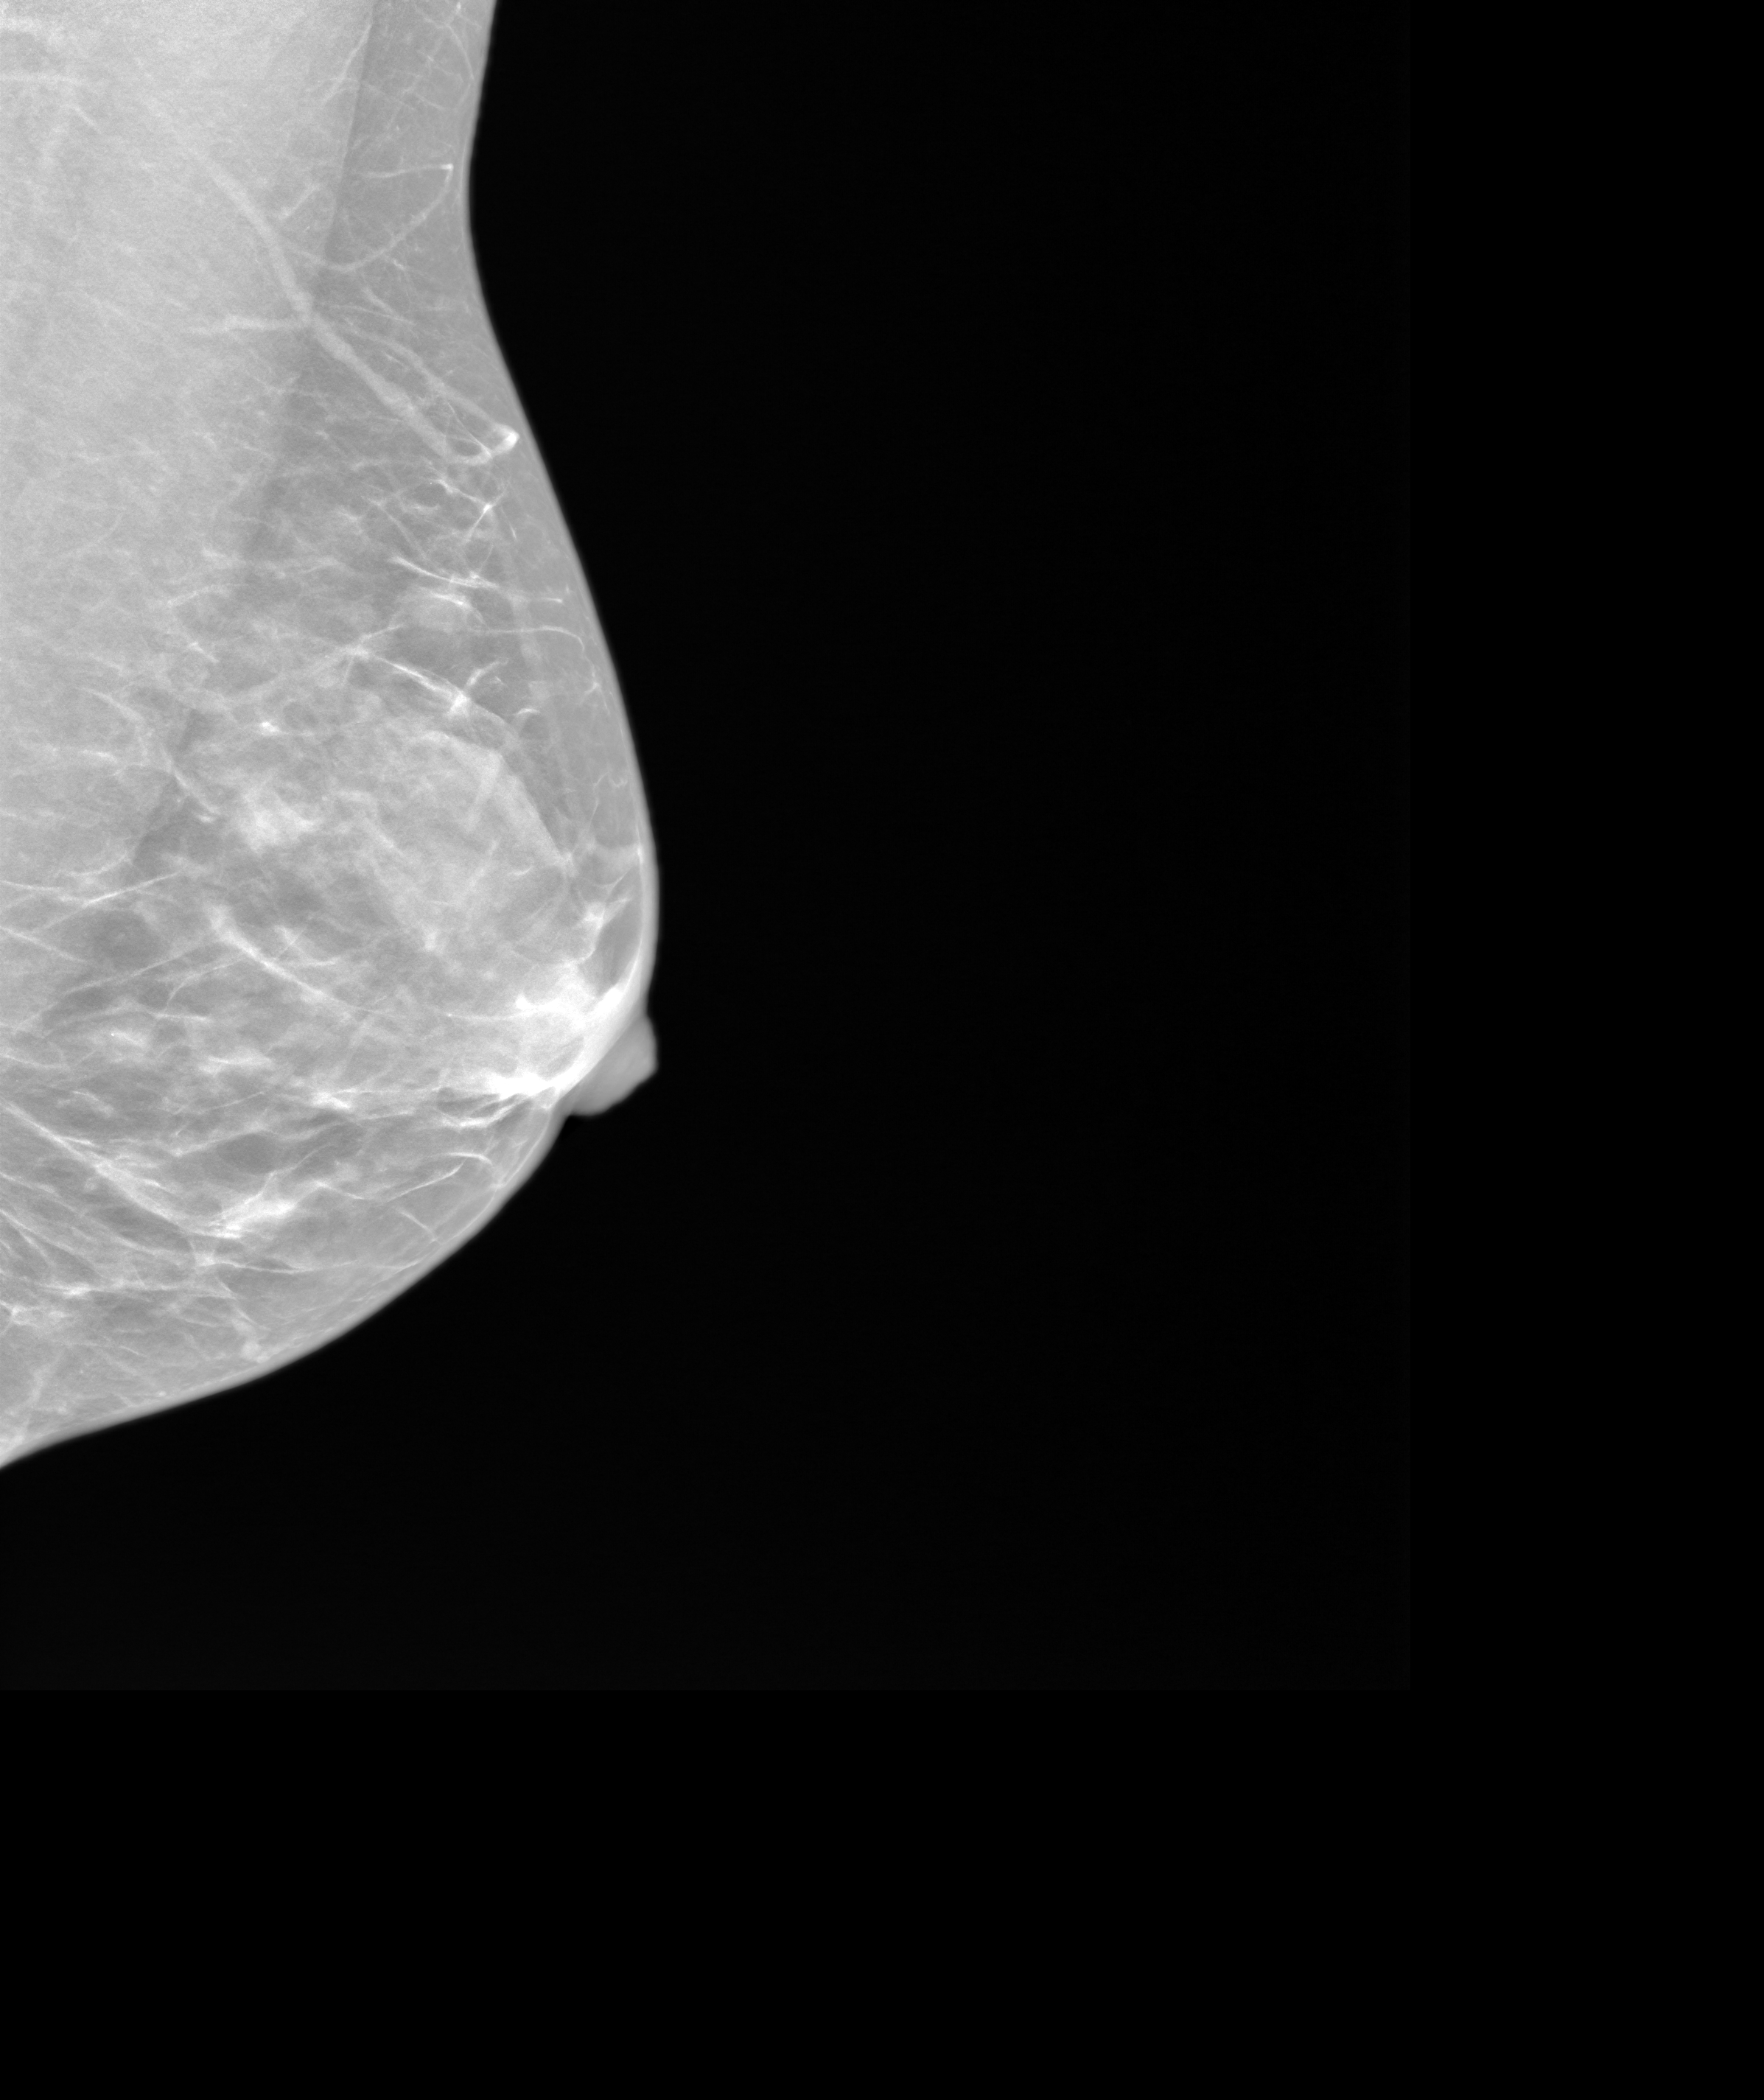
Screening examination; system: SenoIris_1SP1.2(425). Patient aged 49 years (female).
Image type: synthesized 2-D view from tomosynthesis. Breast: left. Projection: mediolateral oblique (MLO) view.